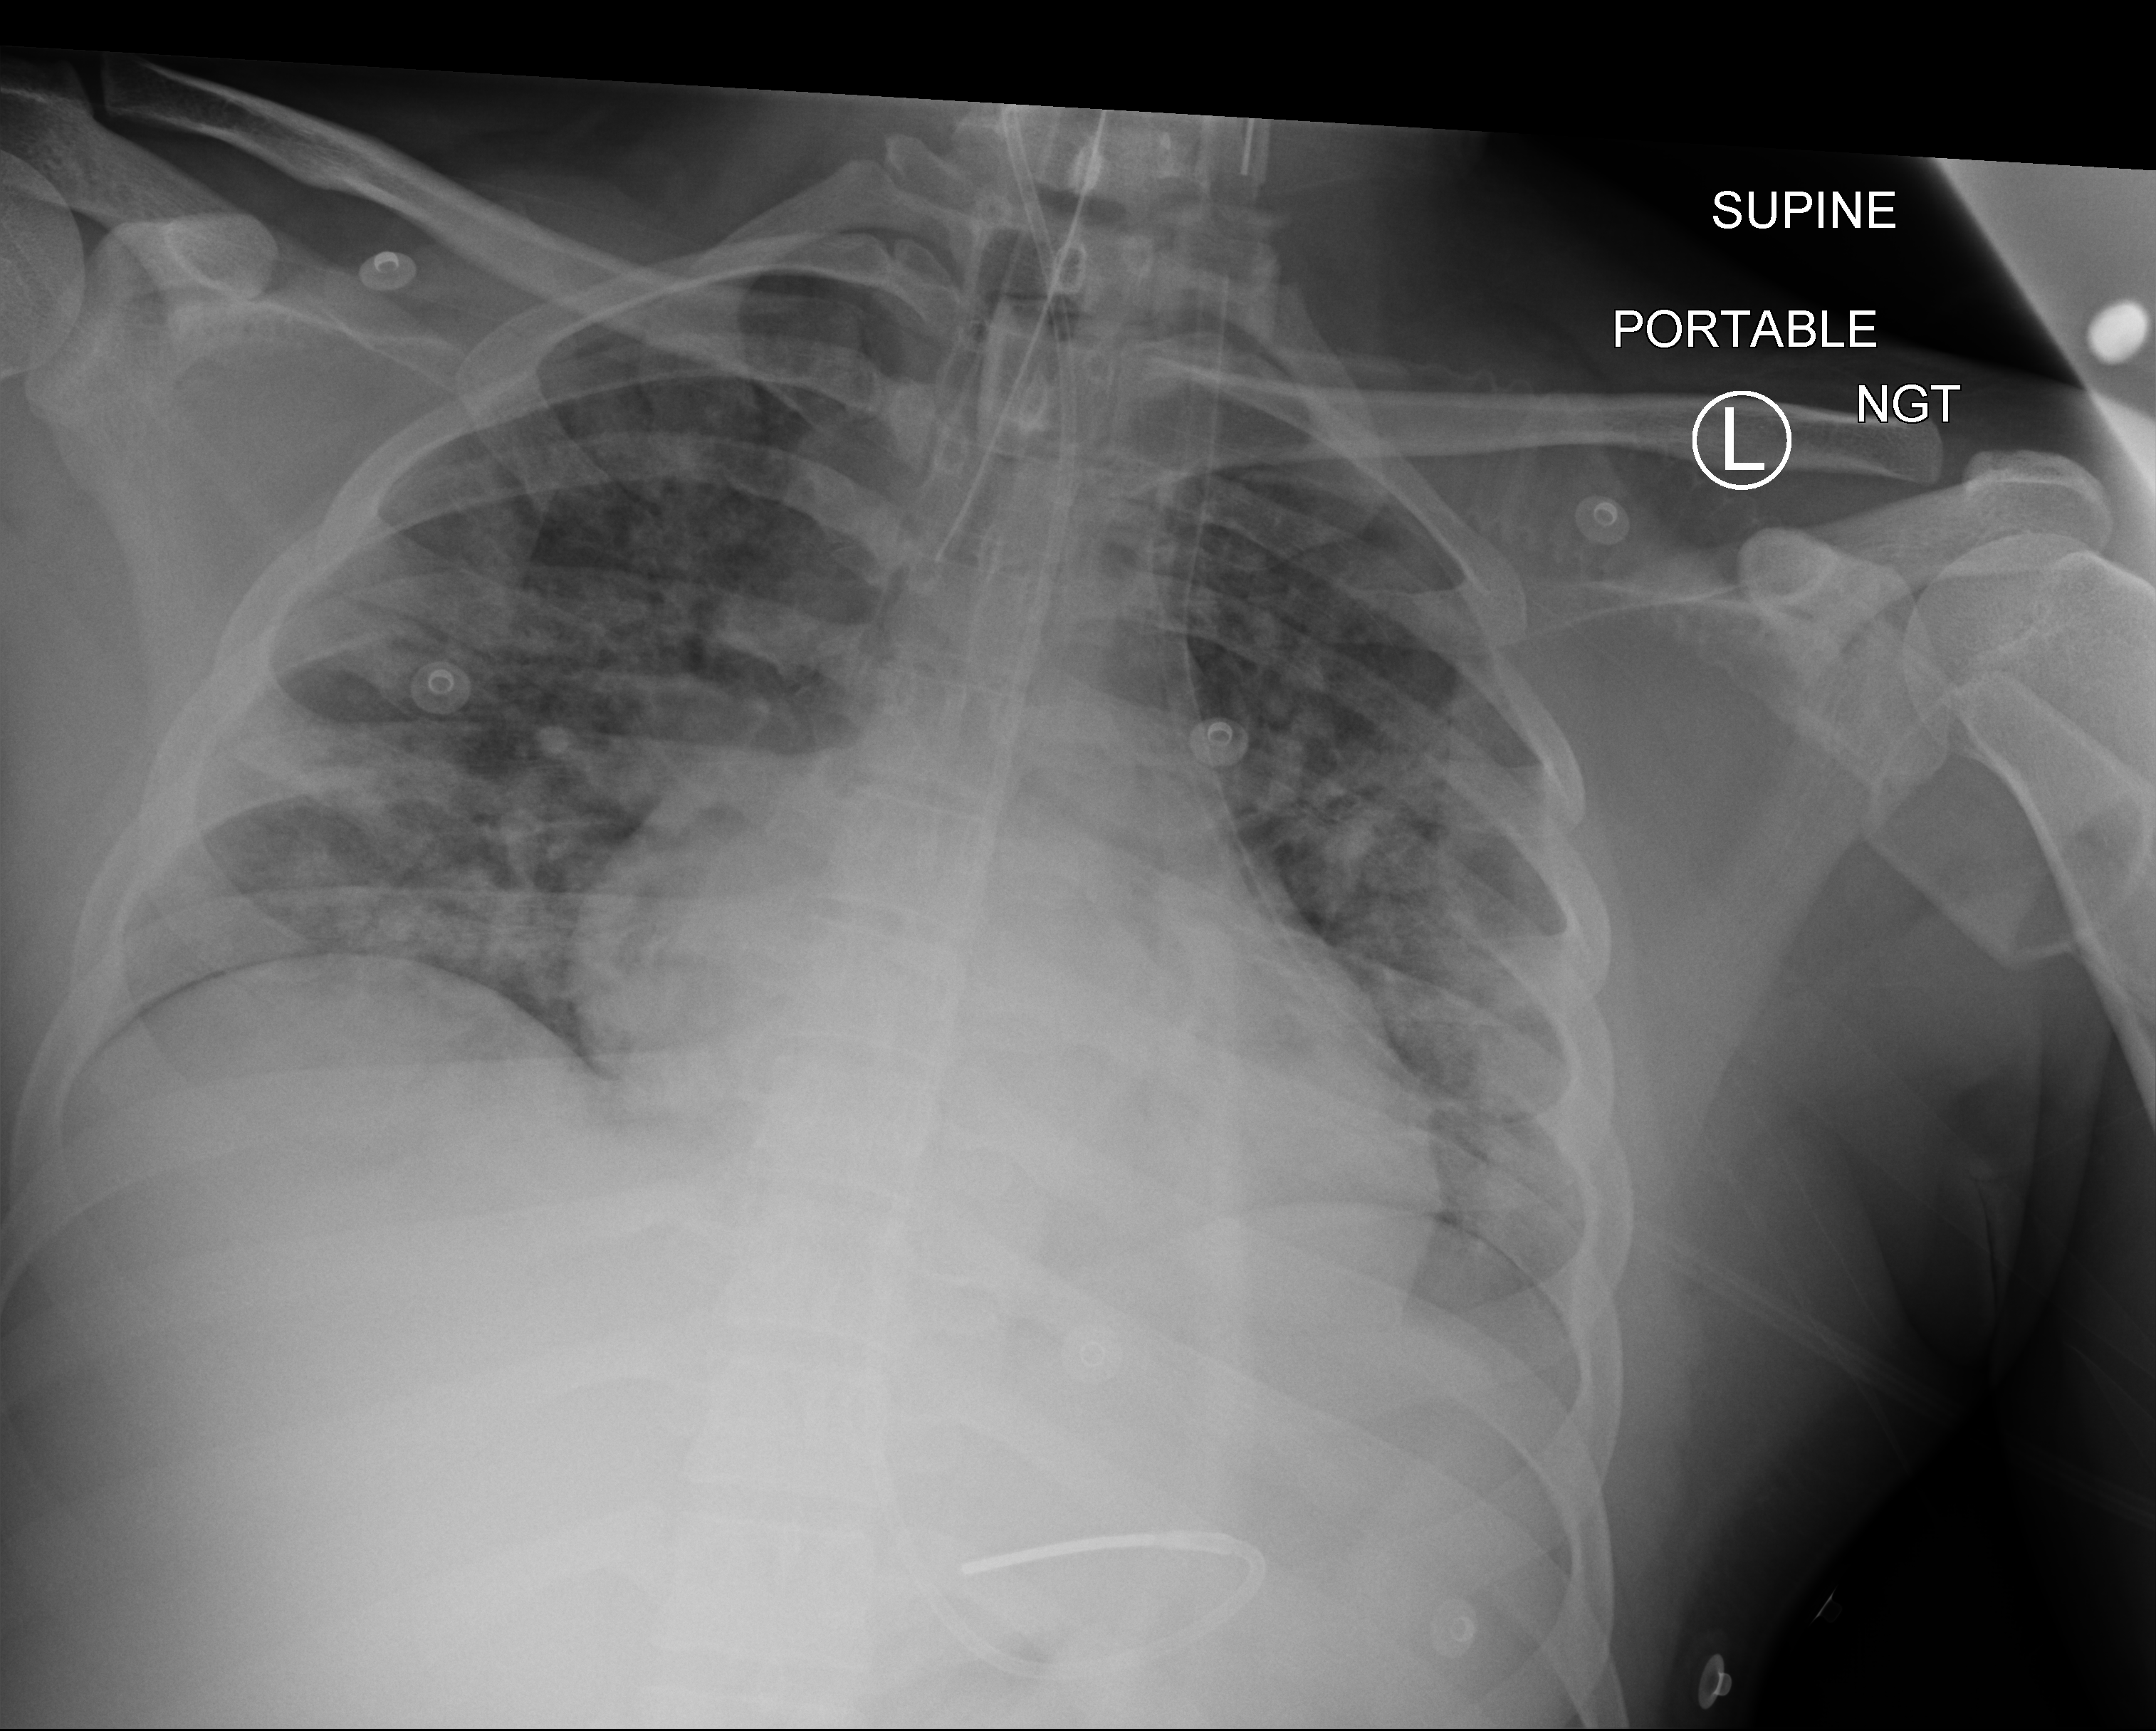
Bedside chest radiograph (computed radiography). Patient hospitalised with COVID-19; male, aged 18–59 years.
From the hospital-stay record, not from the radiograph (when in the stay this image was taken is not recorded): mechanically ventilated during this hospital stay: yes; length of hospital stay: 16 days; admitted to intensive care during this hospital stay: no.